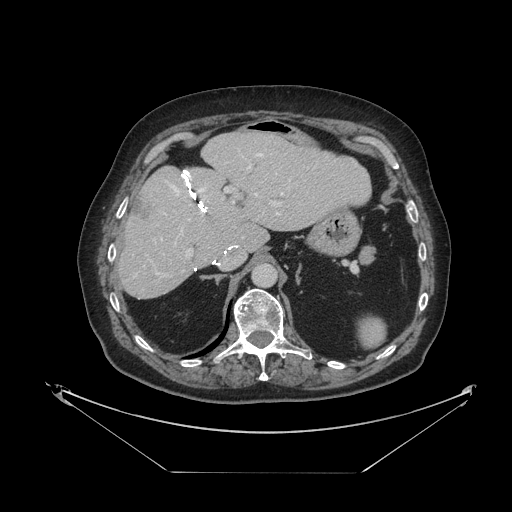
Contrast-enhanced abdominal CT, one axial slice. Position 70 of 121 along the scan axis. Reconstruction kernel STANDARD. 120 kVp. Intravenous contrast given. Soft-tissue window (W 400 / L 40 HU). 2.5 mm slice thickness. 512 × 512 image matrix, field of view 500 × 500 mm. Male patient, age 68 years. Case-level facts recorded for this patient, not image findings: diagnosis: colorectal cancer liver metastases, imaged before liver resection; multiple liver metastases: no; largest metastasis: 4 cm; disease in both lobes: no.
Outlined on this slice (outlined manually by an expert reader):
- hepatic veins: box from (x=161, y=153) to (x=283, y=240) px
- liver: (x=120, y=132)–(x=370, y=299)
- planned liver remnant (the part of the liver to remain after resection): (x=119, y=133)–(x=370, y=299)
- portal vein (with intrahepatic branches): (x=156, y=166)–(x=281, y=277)
- liver metastasis: (x=131, y=196)–(x=154, y=224)